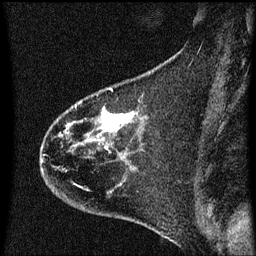
Breast MRI (dynamic contrast-enhanced), one sagittal slice; slice 21 of 60 in the series (ordered by position); dynamic contrast-enhanced series, image 2 of 3 at this slice position (ordered by acquisition); 1.5 T; TE 4.2 ms, TR 8.4 ms; 2 mm slice thickness; 256 × 256 image matrix. Patient: female, 35 years. From the clinical record (not read from this slice): setting: breast cancer imaged before/during neoadjuvant chemotherapy; receptor status: HER2-positive.
Annotated regions visible in this slice (semi-automatically segmented with operator editing):
- analysis volume of interest (the breast-tissue region the enhancement analysis was run in; not a lesion): box from (x=40, y=68) to (x=174, y=173) px
- tumour enhancement mask (voxels above the 70 % enhancement threshold inside the analysis volume of interest): (x=102, y=110)–(x=129, y=141)